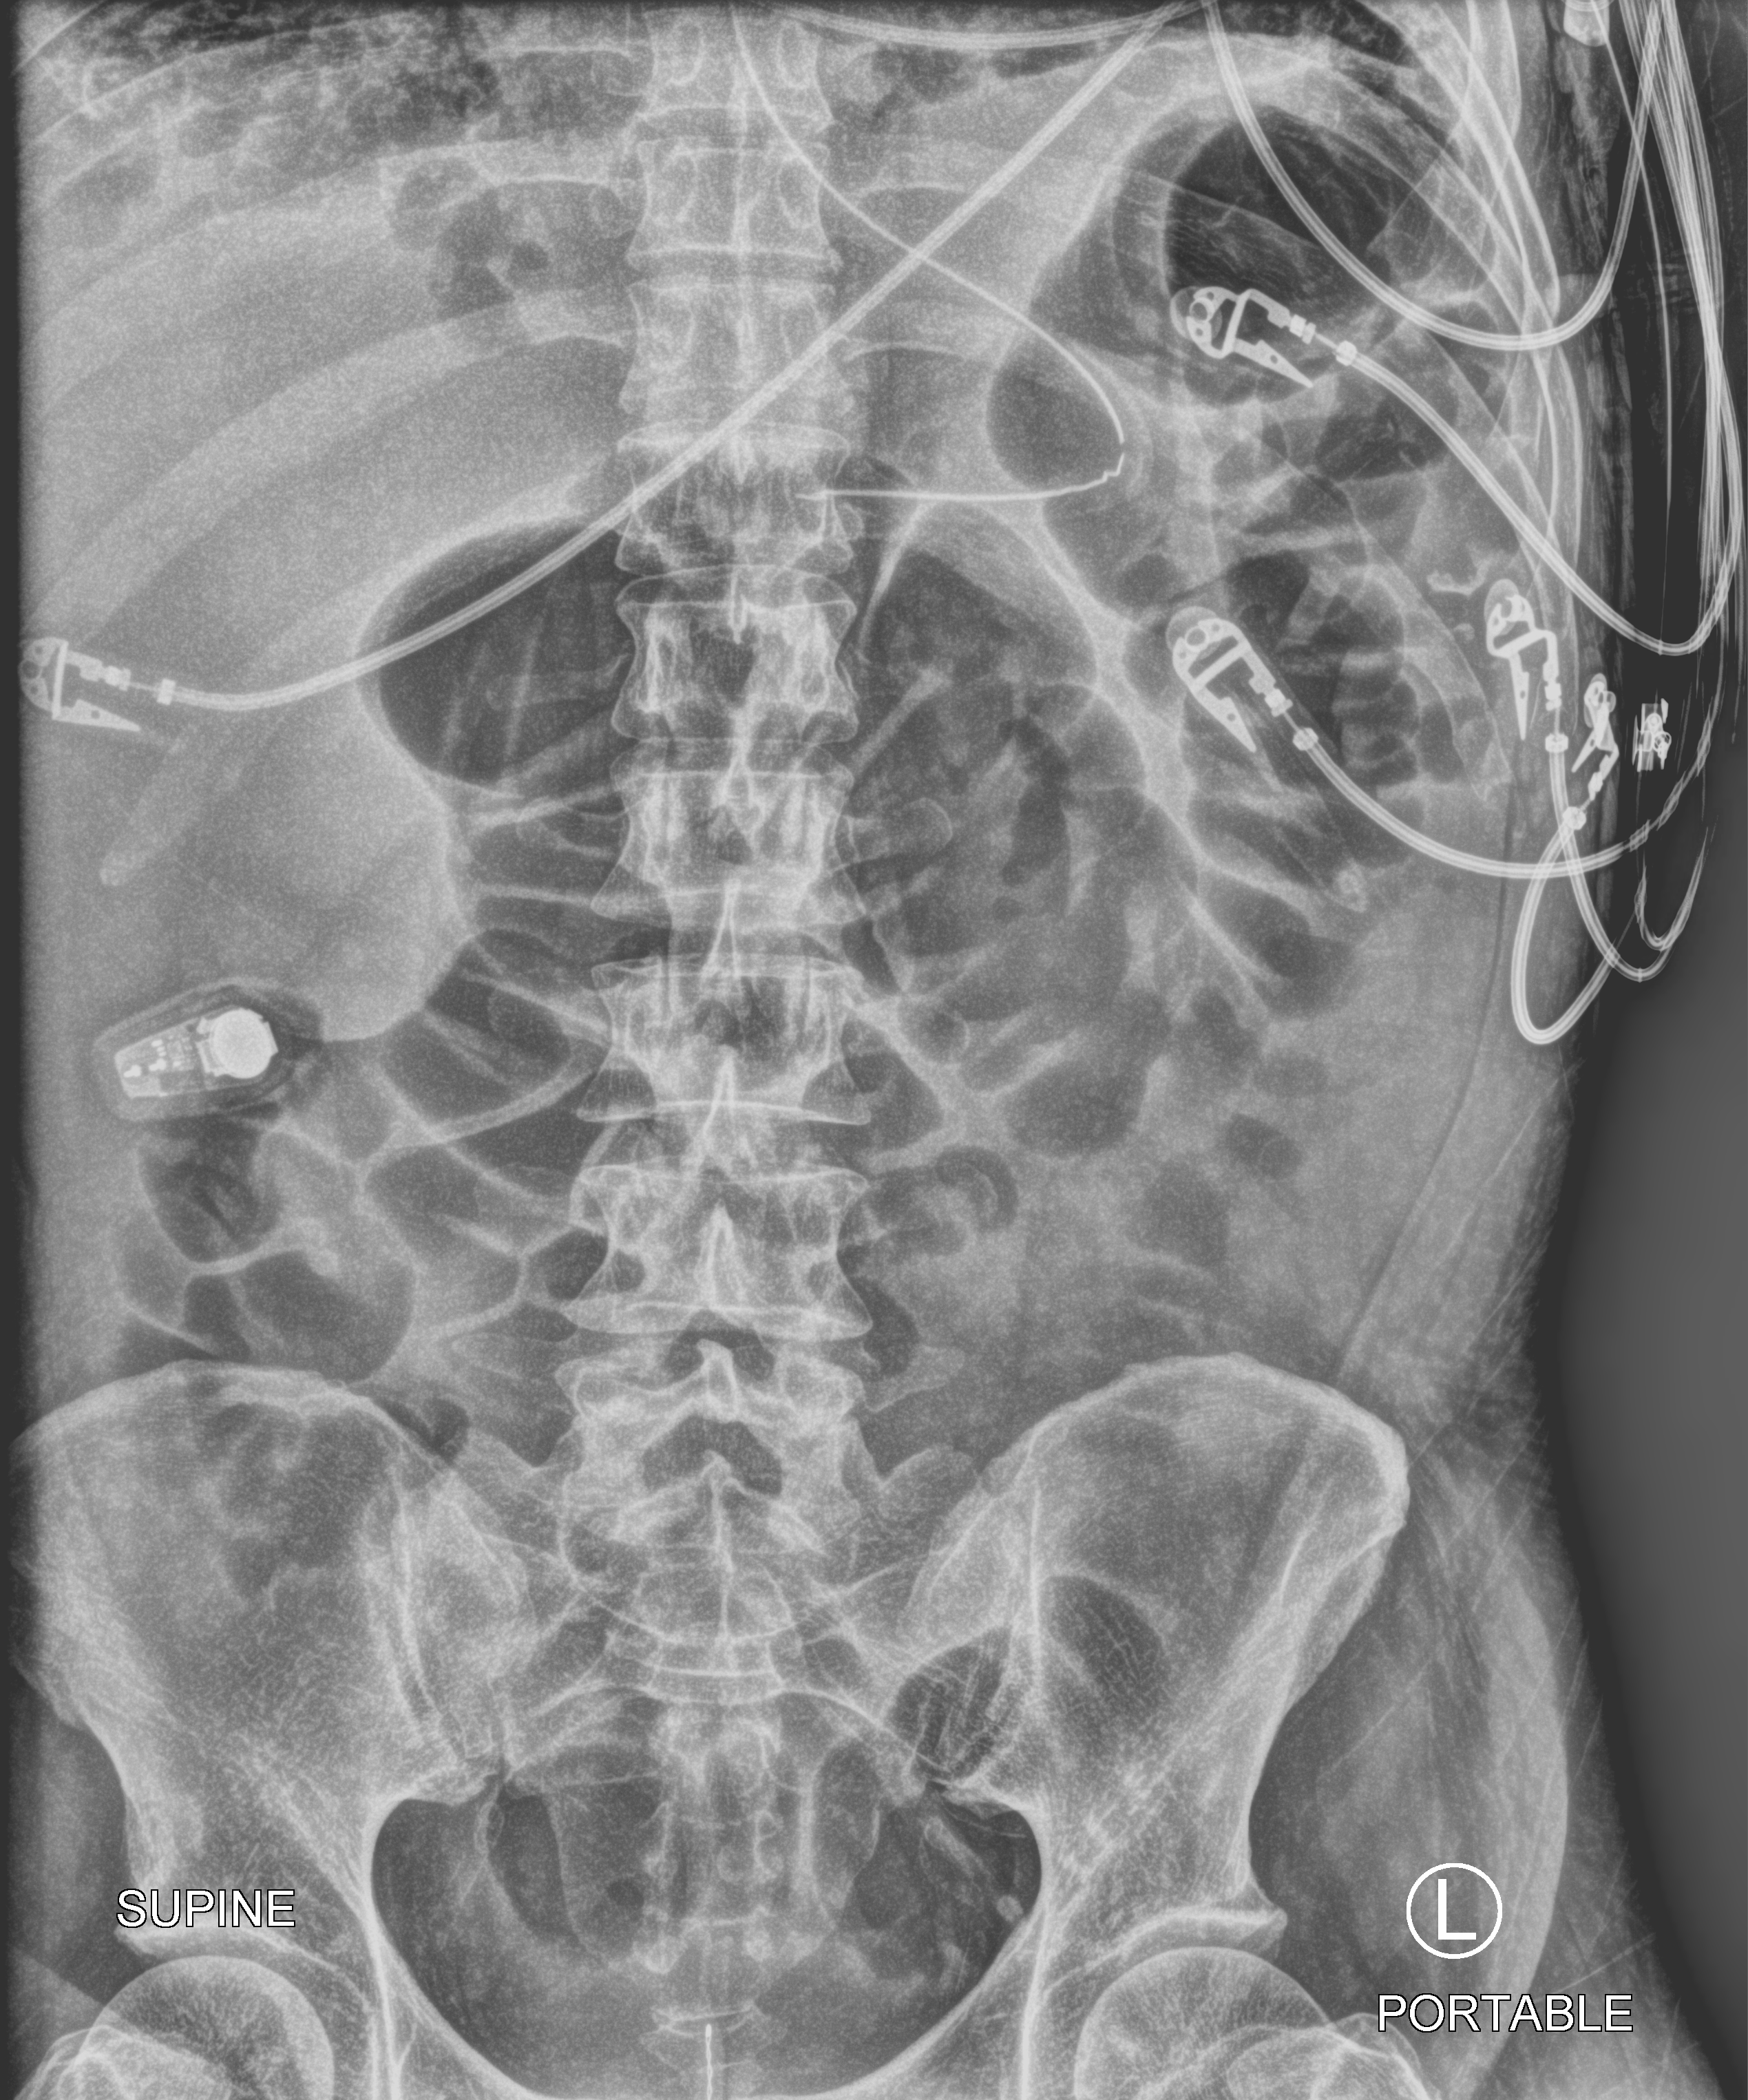
Bedside abdomen radiograph (computed radiography); anteroposterior (AP) projection. Patient hospitalised with COVID-19; male, aged 18–59 years.
From the hospital-stay record, not from the radiograph (when in the stay this image was taken is not recorded):
- length of hospital stay: 96 days